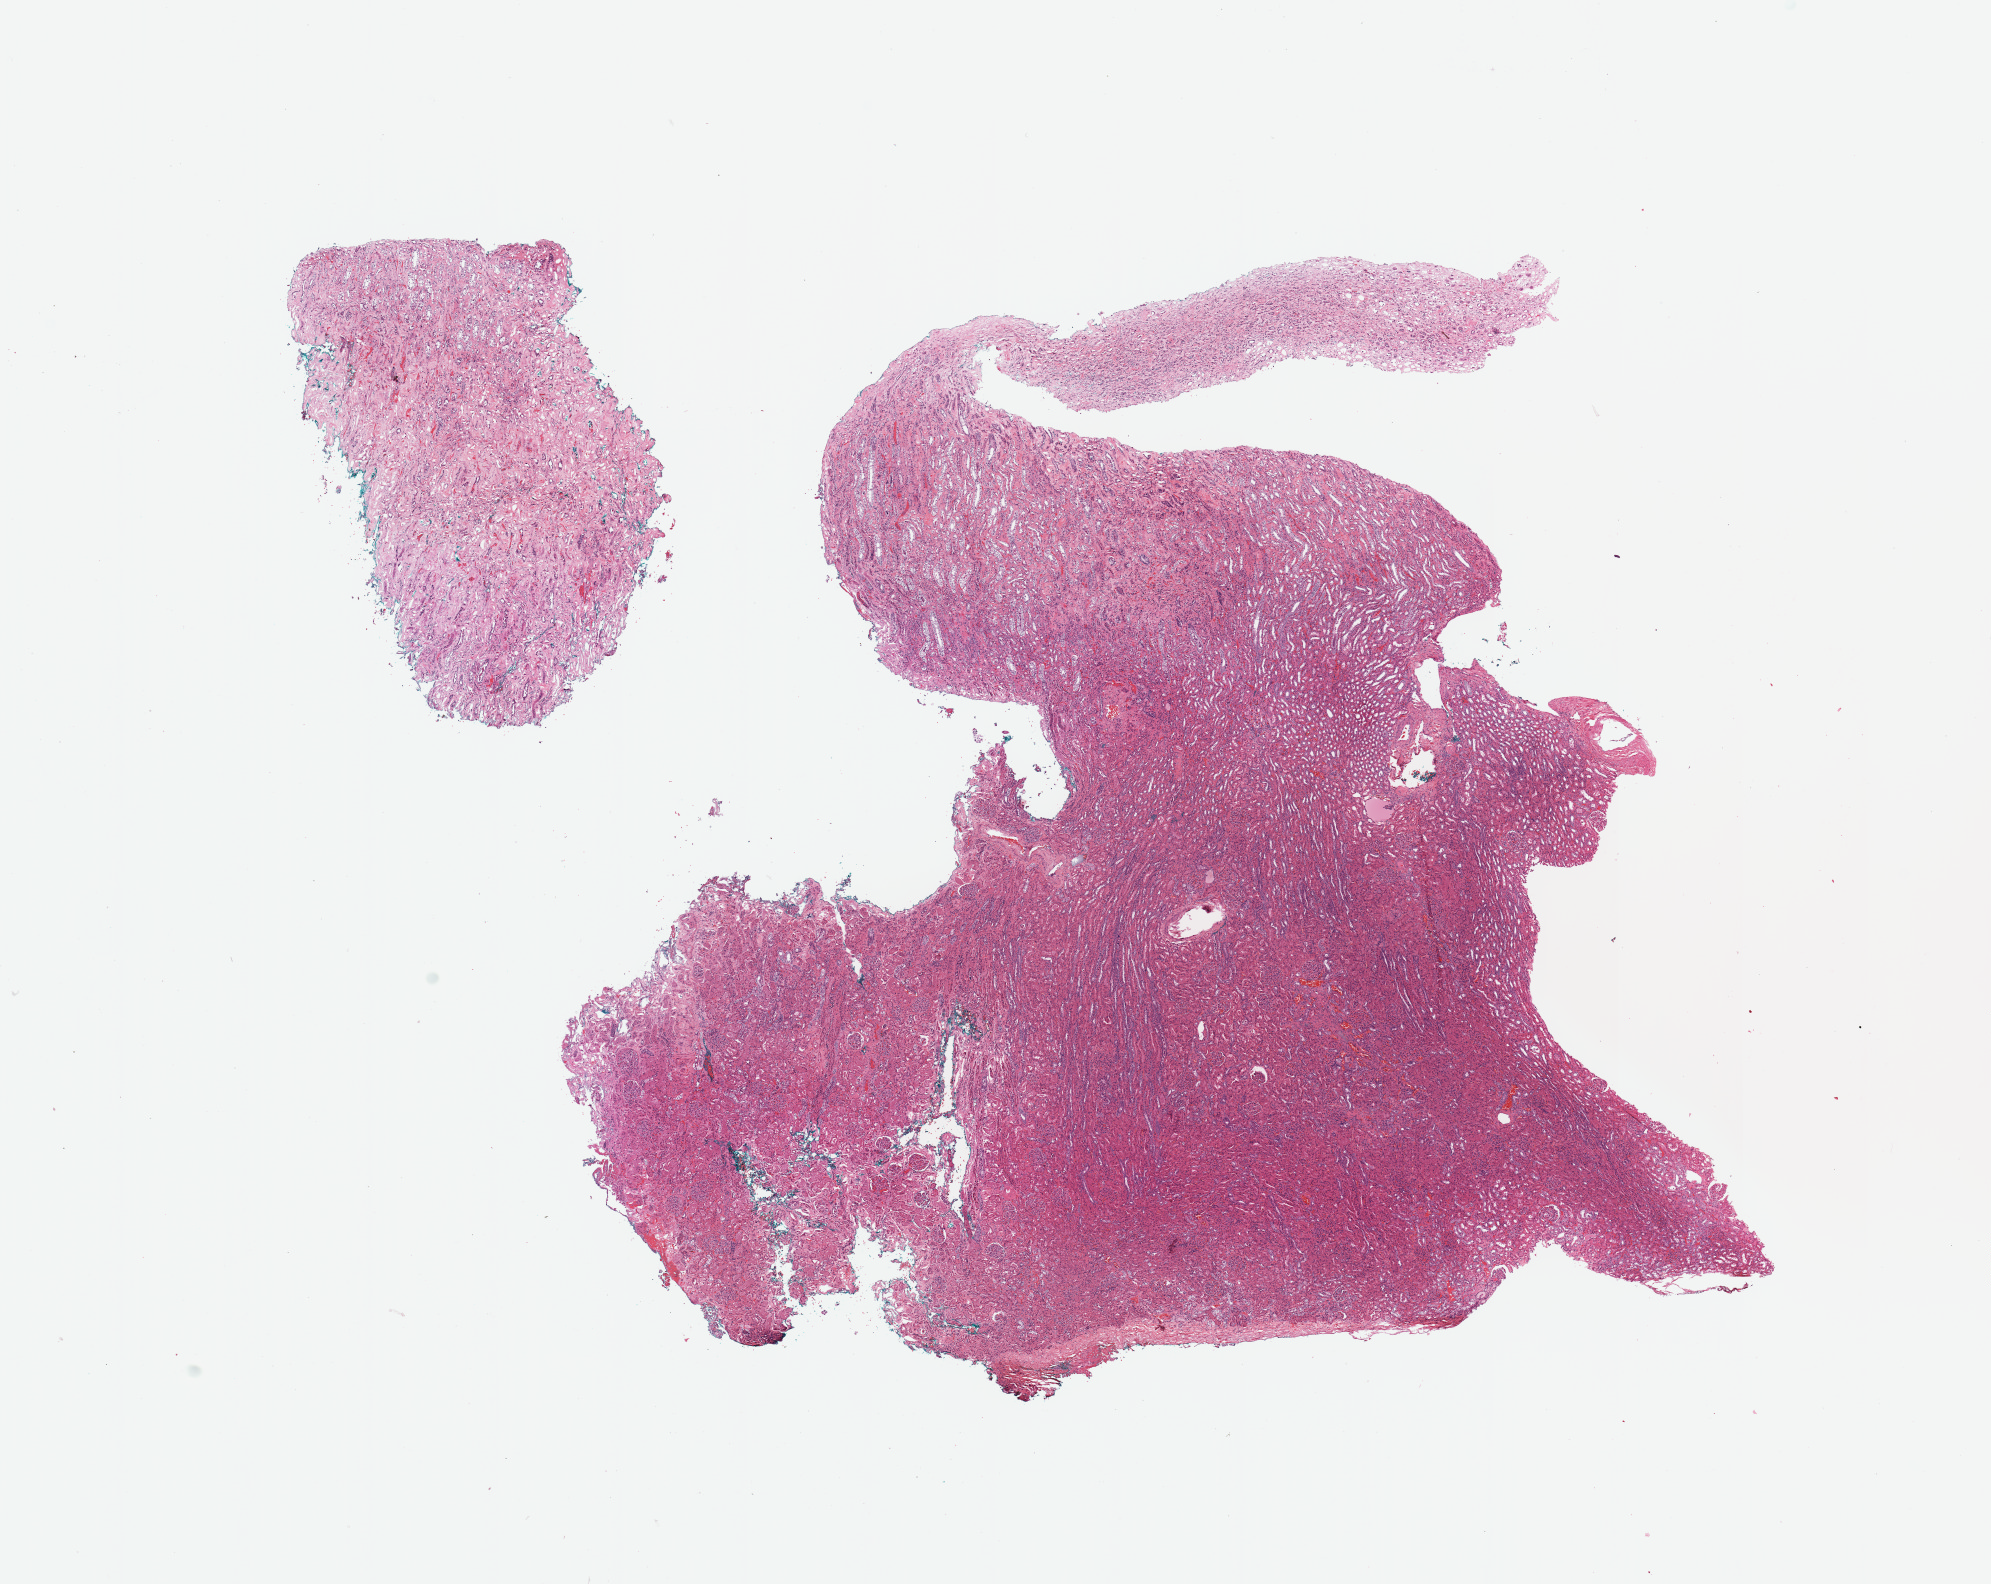
Digitized H&E tissue section (whole slide), low-resolution overview of the scanned area, about 15.8 x 12.5 mm (acquisition: 20x scan), normal (non-tumour) tissue sample, kidney. Patient: male, age 63 years.
- this section: normal (non-tumour) tissue from the same patient
- patient diagnosis: Renal cell carcinoma, NOS